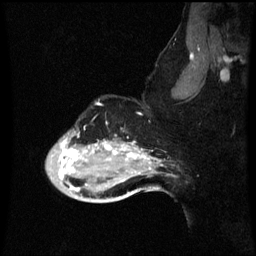
Breast MRI (dynamic contrast-enhanced), one sagittal slice. Position 47 of 60 along the scan axis. Dynamic contrast-enhanced series, image 2 of 3 at this slice position (ordered by acquisition). 1.5 T. TE 4.2 ms, TR 8.9 ms. 2 mm slice thickness. 256 × 256 image matrix, field of view 200 × 200 mm. Female patient, age 49 years. Case-level facts recorded for this patient, not image findings: setting: breast cancer imaged before/during neoadjuvant chemotherapy; receptor status: HR-positive, HER2-negative.
Annotated regions visible in this slice (semi-automatically segmented with operator editing):
- analysis volume of interest (the breast-tissue region the enhancement analysis was run in; not a lesion): box from (x=46, y=128) to (x=159, y=199) px
- tumour enhancement mask (voxels above the 70 % enhancement threshold inside the analysis volume of interest): (x=60, y=140)–(x=147, y=191)